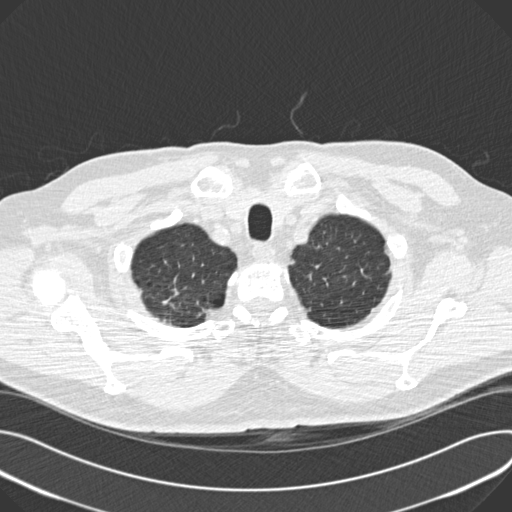
Low-dose screening chest CT, one axial slice. Position 161 of 180 along the scan axis. Reconstruction kernel B30f. Lung window (W 1500 / L -600 HU). 2 mm slice thickness. 512 × 512 image matrix, field of view 376 × 376 mm.
Annotated regions visible in this slice (manually delineated by an expert):
- lesion 1 (tumor, upper lobe of right lung): box from (x=206, y=309) to (x=217, y=318) px